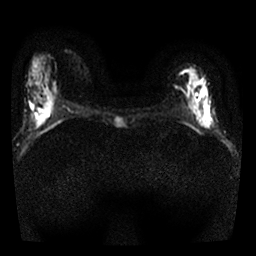
Breast MRI, one axial slice; position 7 of 25 along the scan axis; diffusion-weighted series; image 2 of 4 stored at this slice position (different b-values; order by instance number); 1.5 T; 256 × 256 image matrix, field of view 300 × 300 mm. Female patient.
Annotated regions visible in this slice (outlined manually by an expert reader):
- tumour on diffusion-weighted imaging: bounding box <185,86,213,129> (left, top, right, bottom; pixels)